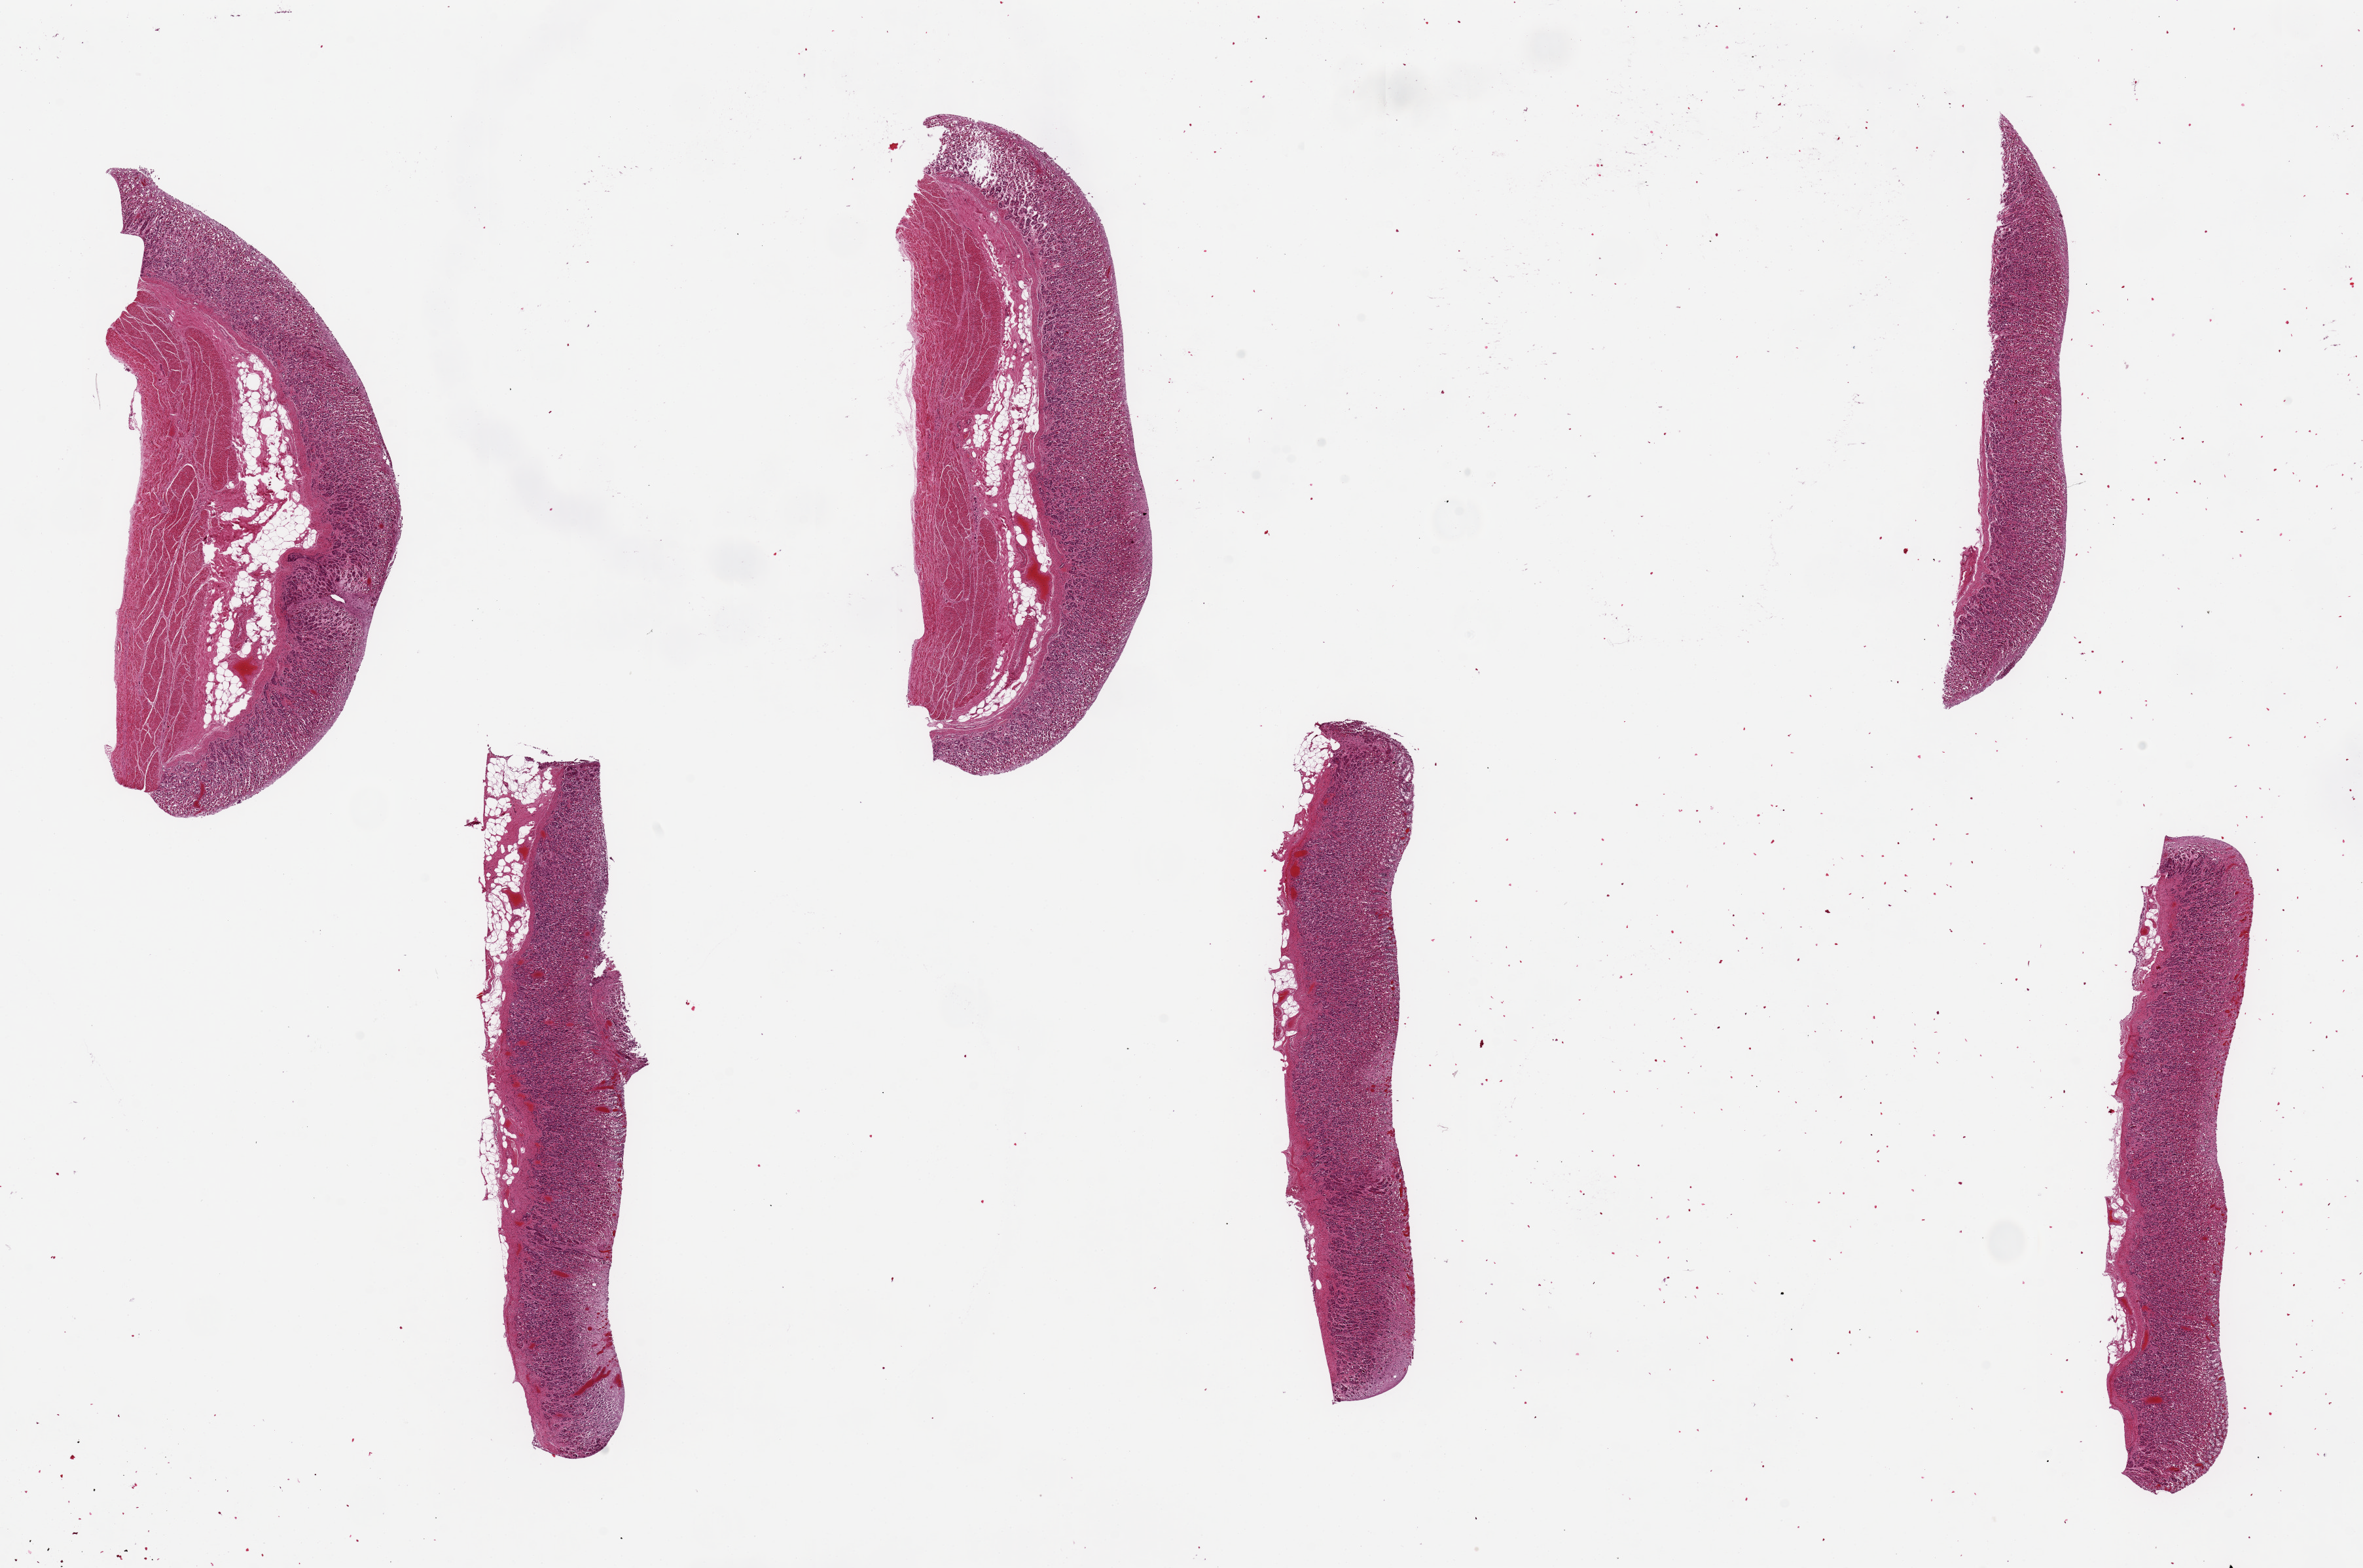
H&E whole-slide image, low-resolution overview of the scanned area, about 28.5 x 18.9 mm; PAXgene-fixed paraffin-embedded (PFPE) section; section of stomach (target tissue); donor tissue sample. Donor: male.
• pathologist's review note for this sample: 6 pieces, up to 9x2mm; mucosa 40-100% thickness, moderately--poorly preserved